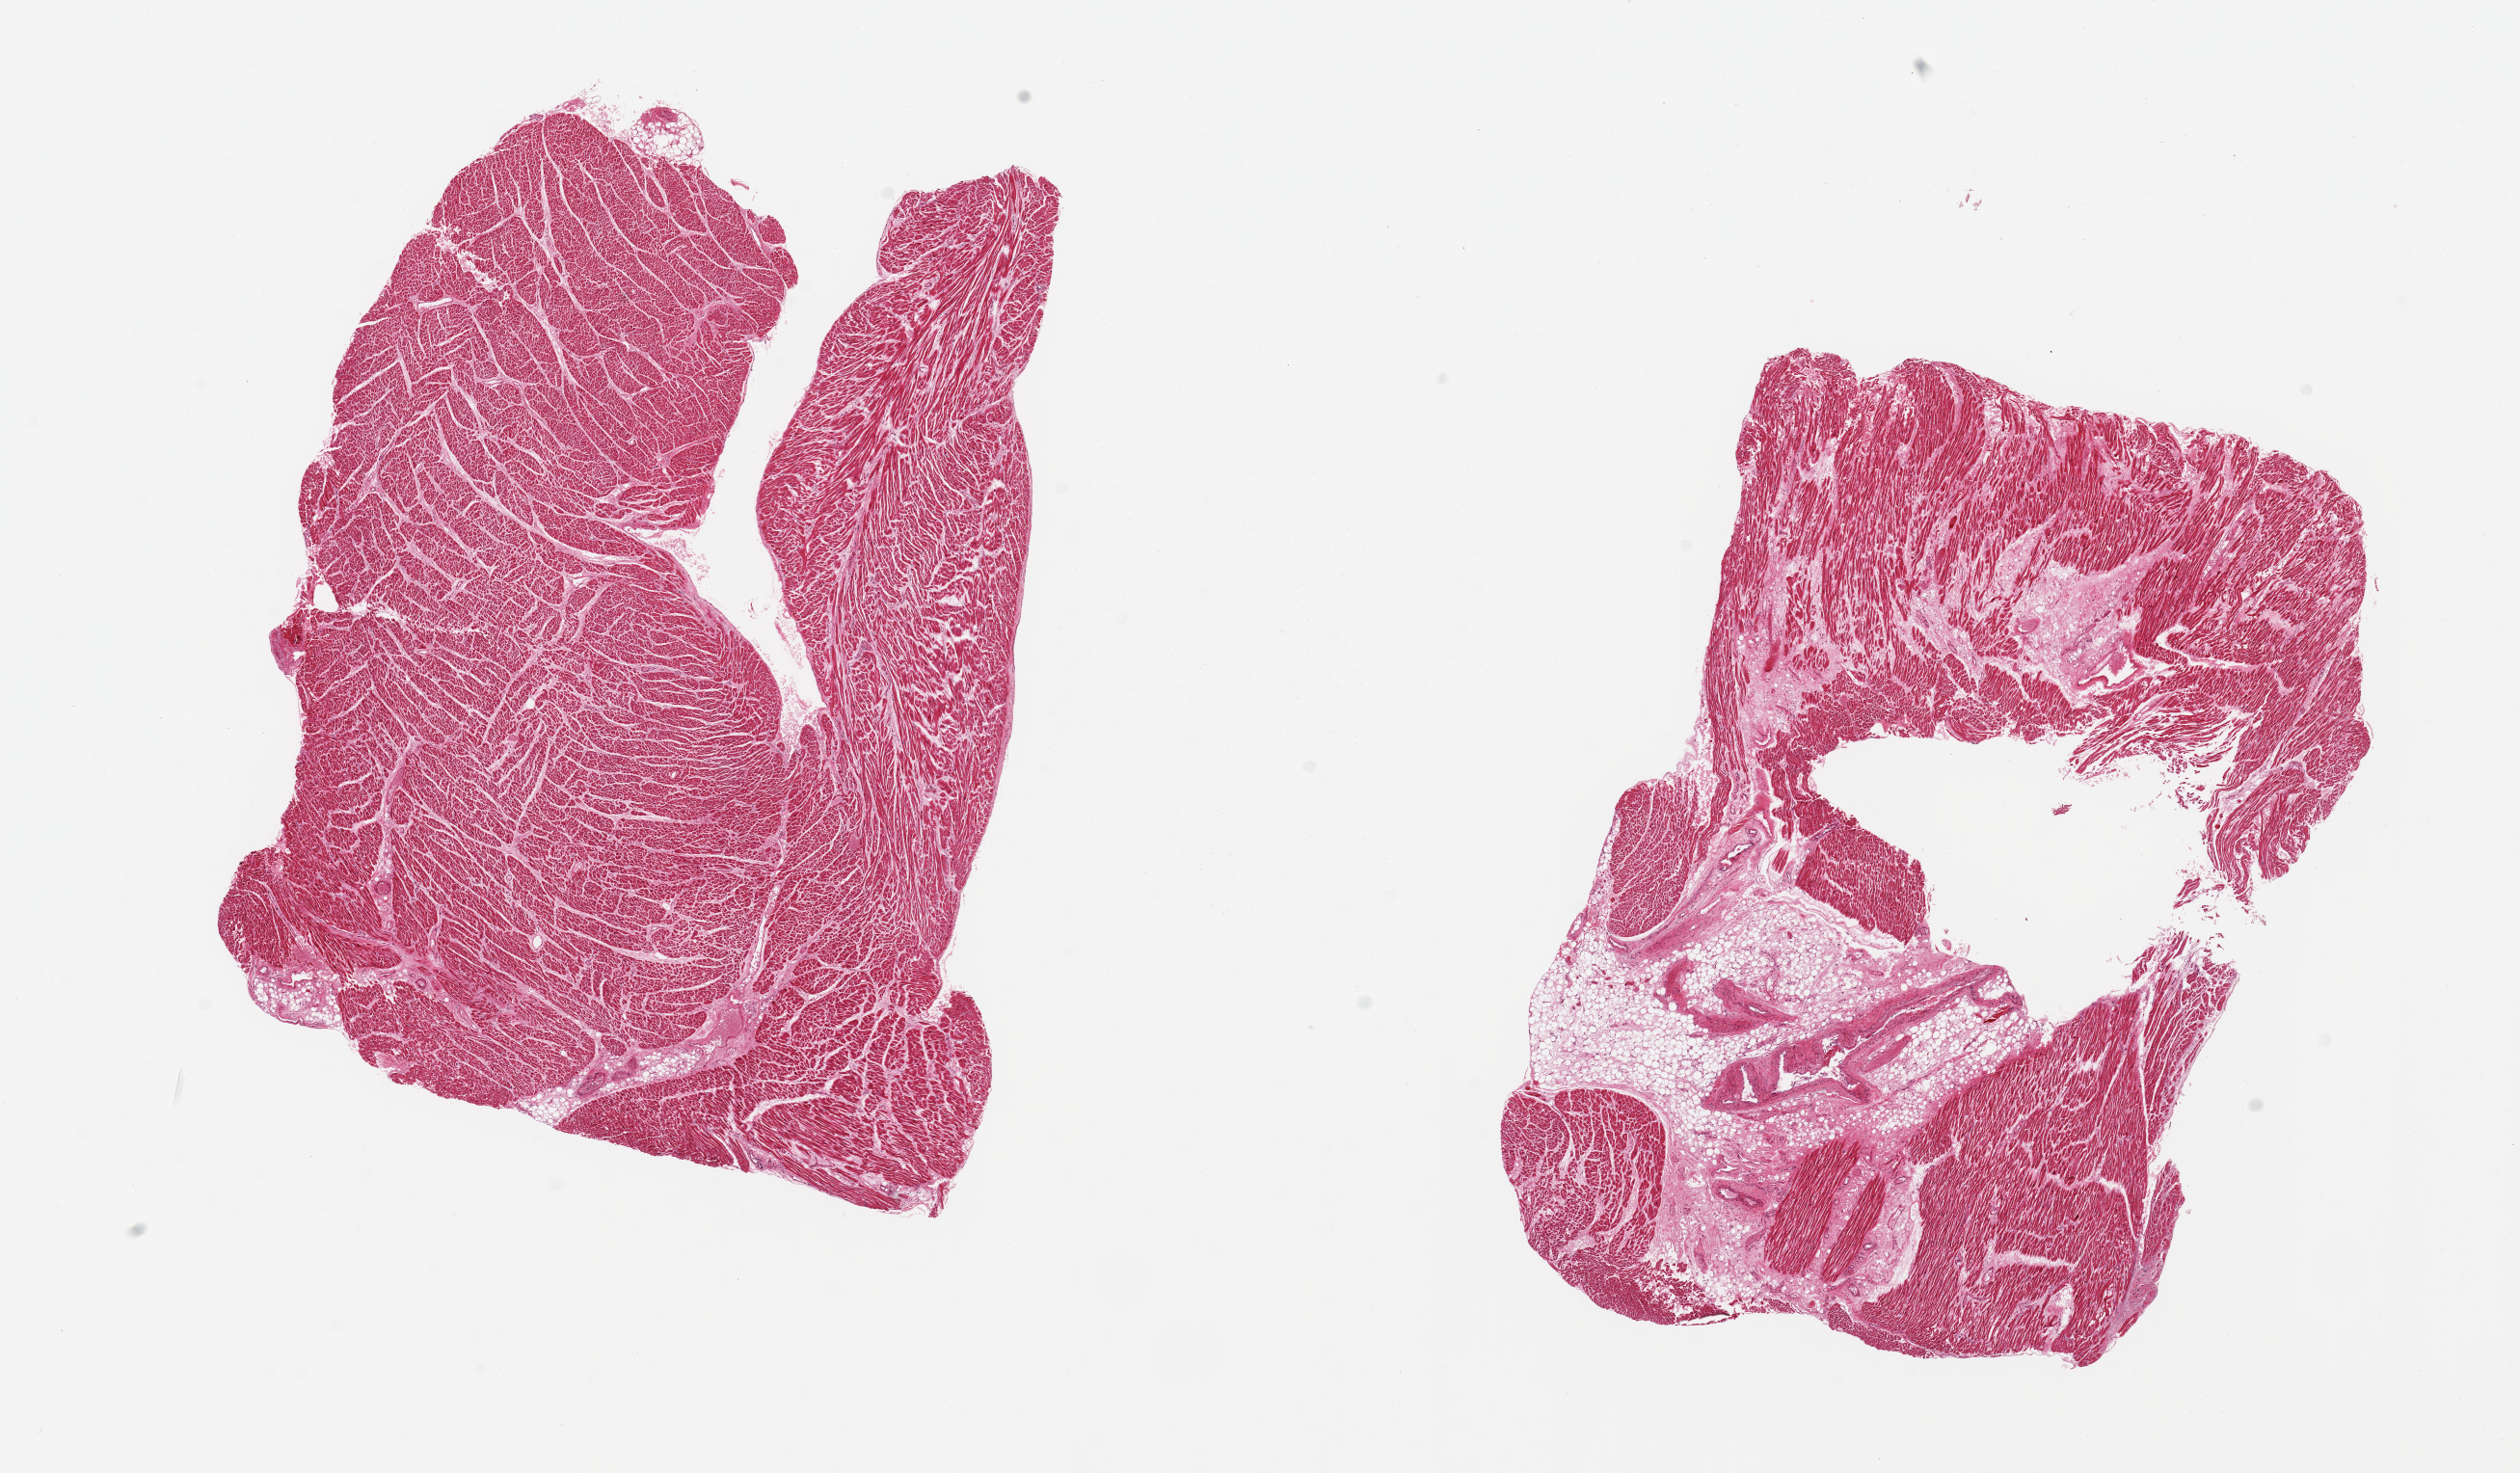
Whole-slide image, H&E stain, whole scanned area (about 20.7 x 12.1 mm, from a 20x scan) shown as a low-resolution overview, PAXgene-fixed, paraffin-embedded tissue, section of heart (target tissue), tissue donor sample.
- pathologist's review note for this sample: 2 pieces 9x6.5 & 8x6.5mm; poorly preserved, apparent fibrotic focus